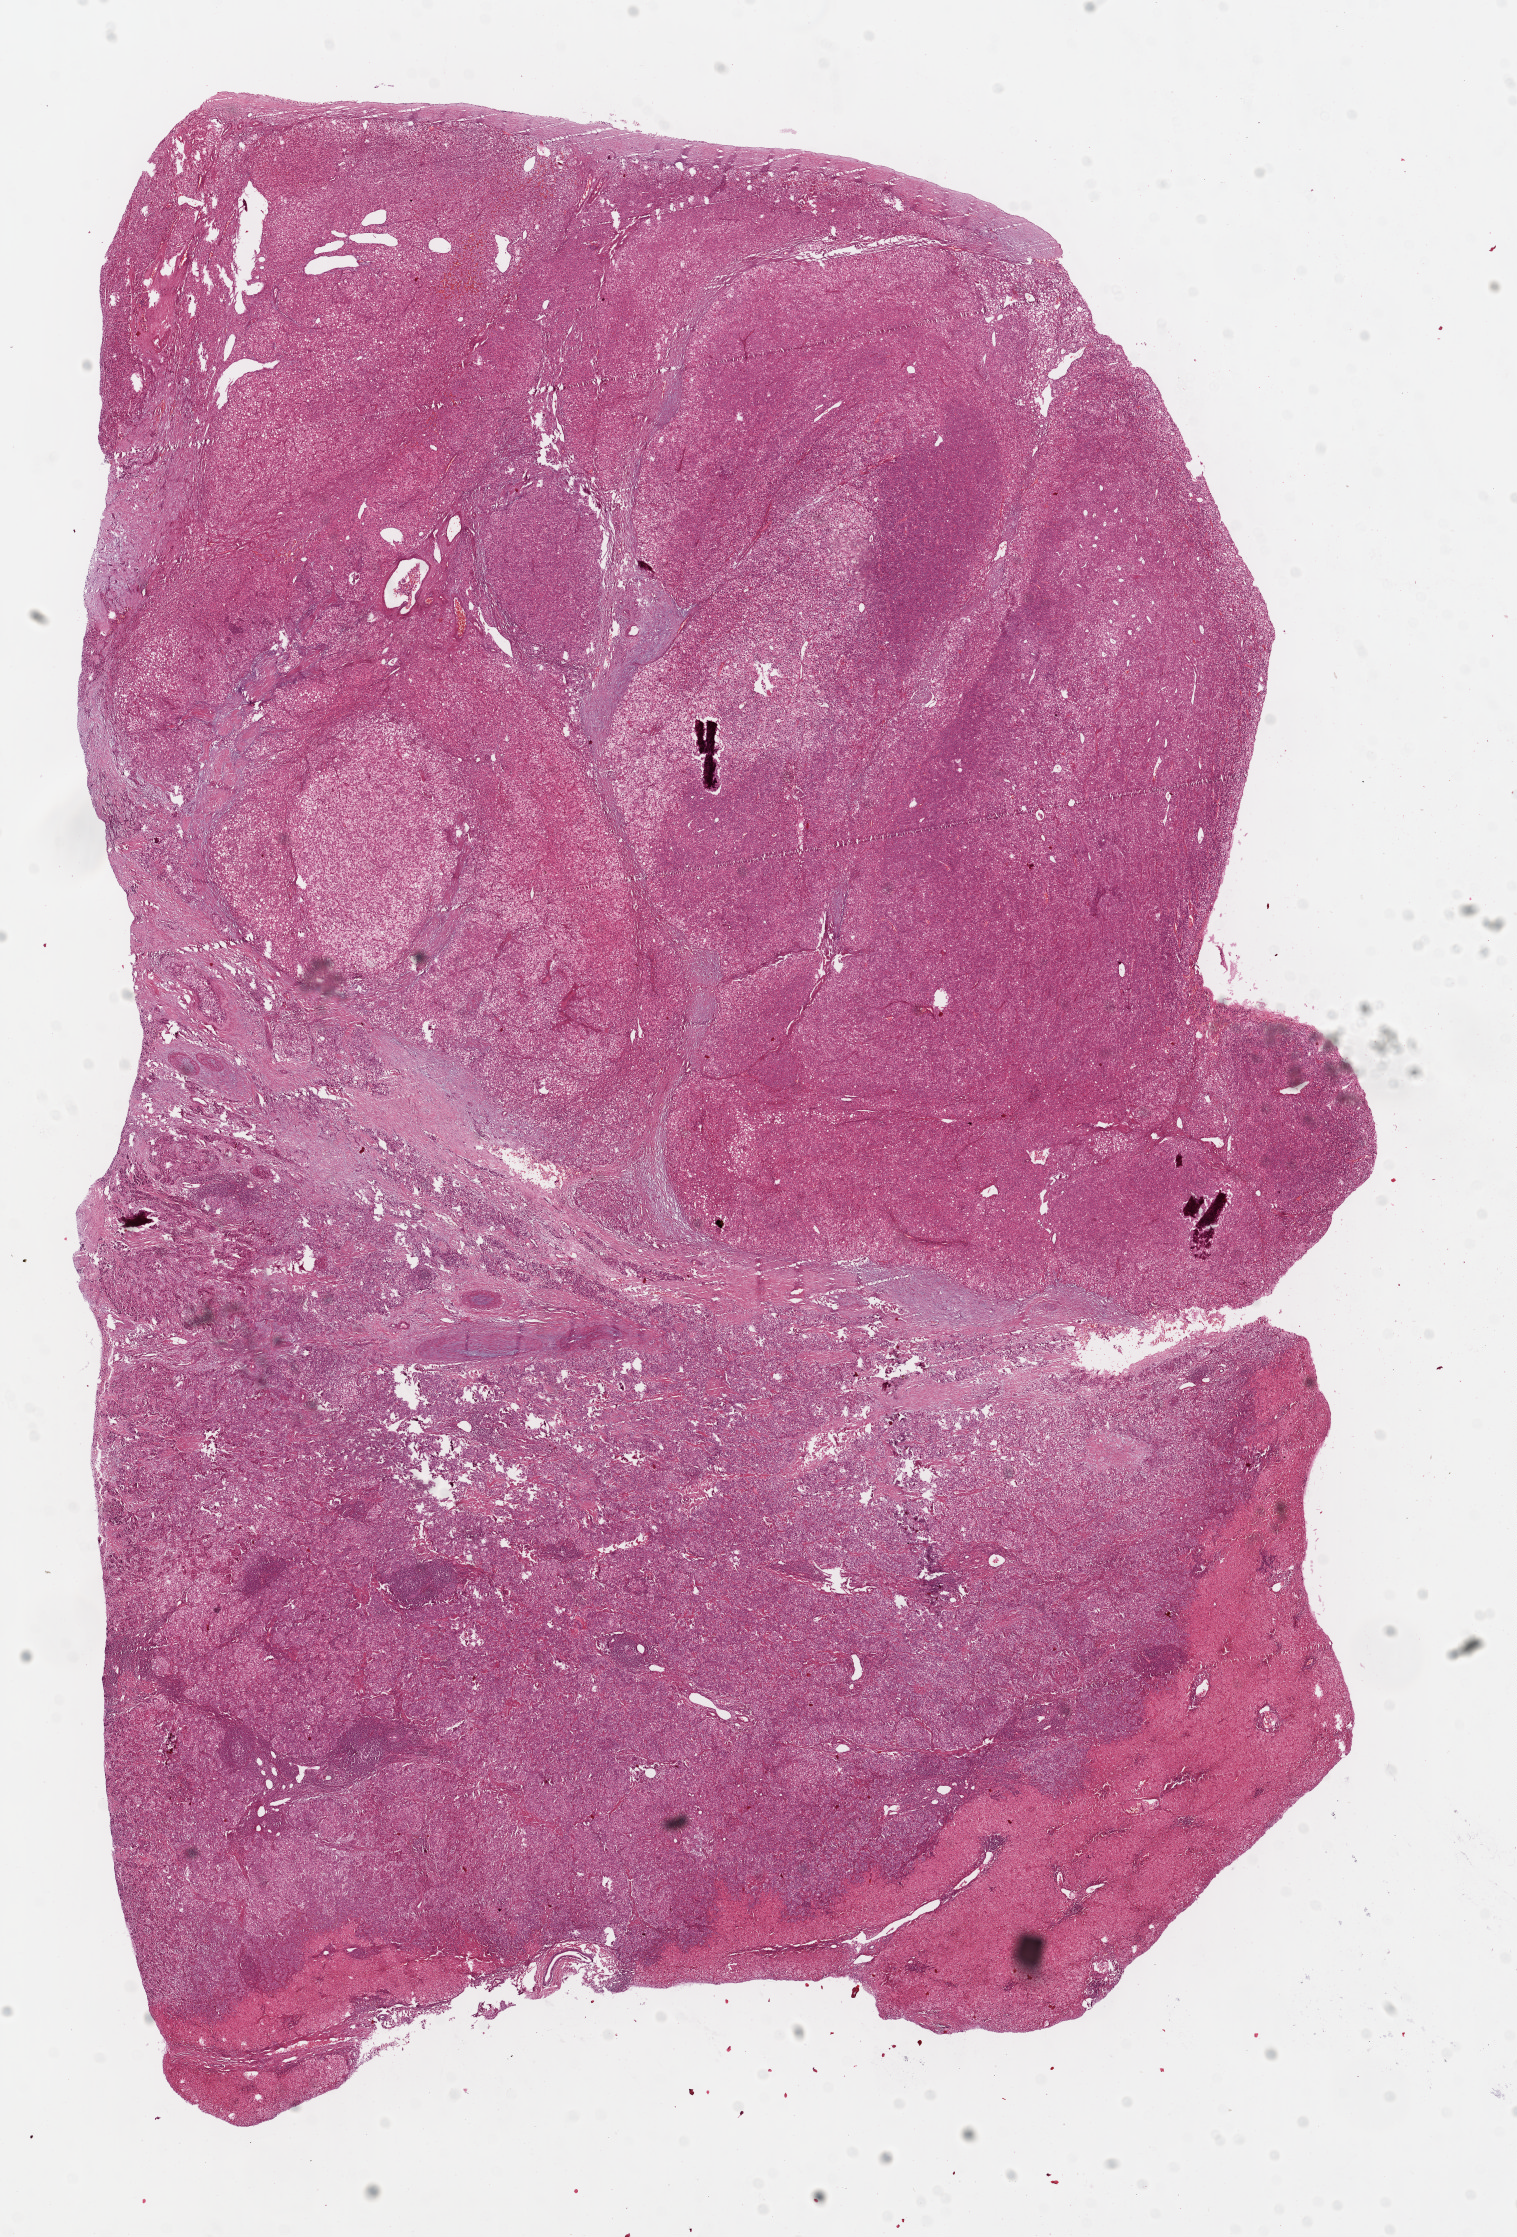
Digitized H&E tissue section (whole slide), low-resolution overview of the scanned area, about 11.9 x 17.6 mm; FFPE section; primary tumour sample from the liver. Male patient; age at initial diagnosis 44 years. Histologic grade: G2 (moderately differentiated).
• AJCC pathologic stage: II
• TNM: T2 N0 M0
• histologic diagnosis: Hepatocellular carcinoma, NOS